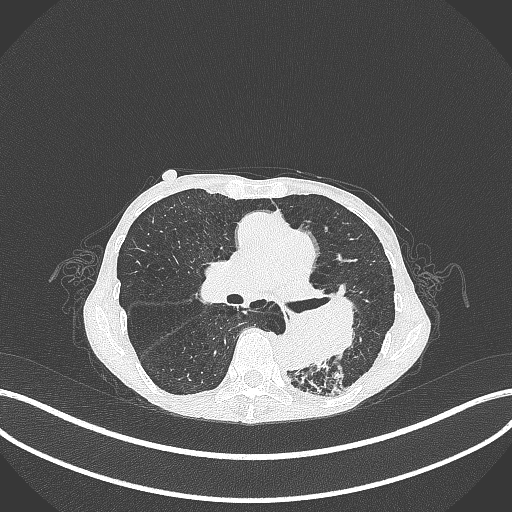
Chest CT, one axial slice. Position 154 of 347 along the scan axis. Reconstruction kernel B70f. 120 kVp. Lung window (W 1500 / L -600 HU). 512 × 512 image matrix, field of view 400 × 400 mm. Female patient, age 70 years. From the clinical record (not read from this slice): clinical TNM (as recorded): T3 N0 M0; histopathological grade: G3.
Annotated regions visible in this slice (rectangle marked by the reading radiologist):
- lung tumour (recorded histology: small cell carcinoma): box from (x=265, y=293) to (x=358, y=371) px